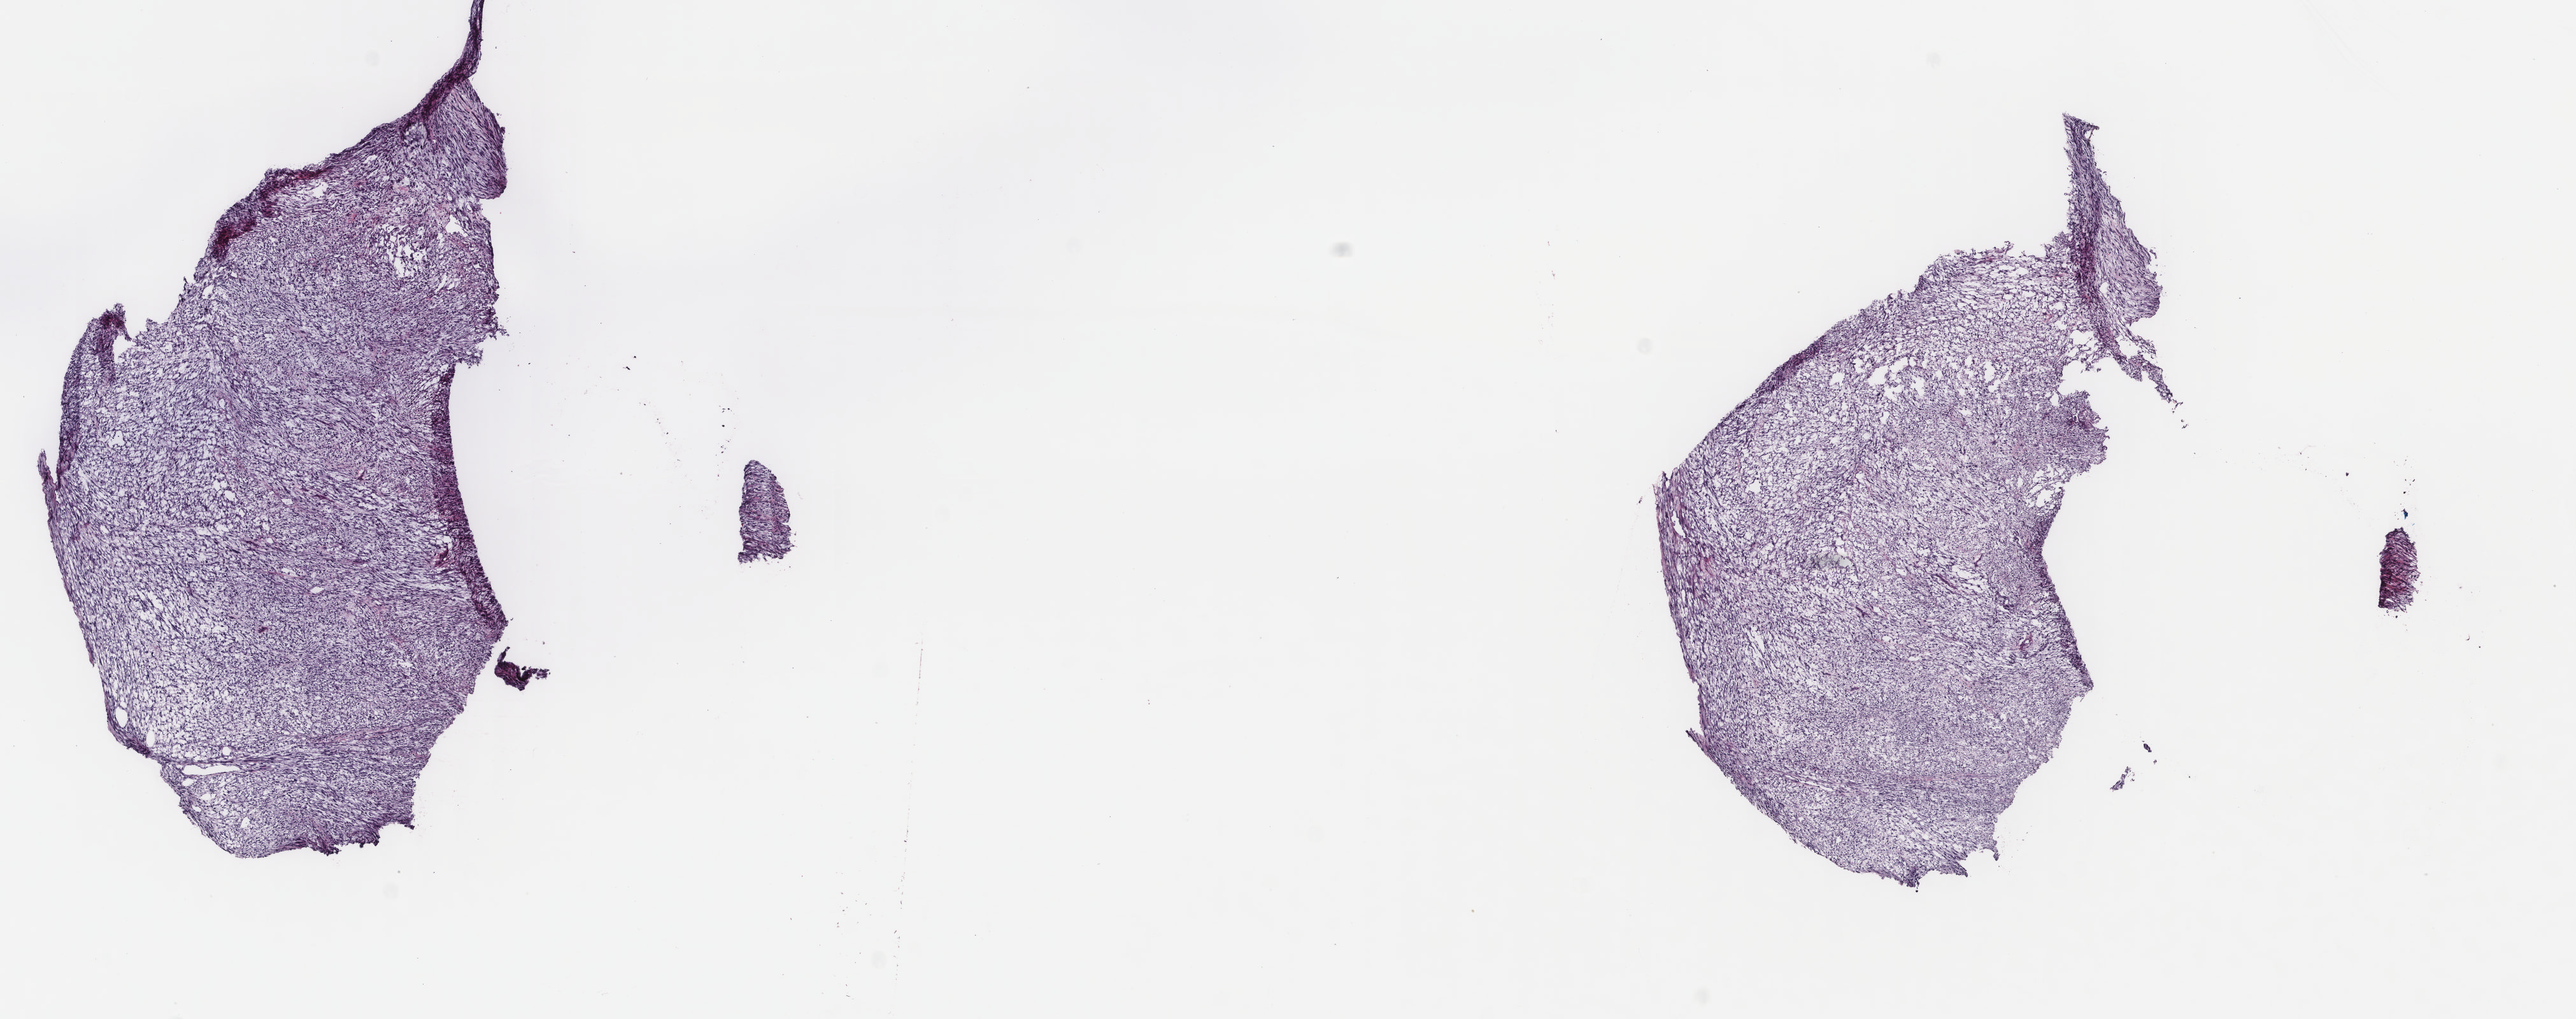
Digitized H&E-stained tissue section (whole slide) — whole scanned area (about 16.1 x 6.4 mm, slide scanned at 40x) shown as a low-resolution overview; frozen section from the top of the tissue portion; retroperitoneum and peritoneum, primary tumour sample. Female, age 65 years at initial diagnosis. Slide review estimates, as recorded: tumour cells 95%, tumour nuclei 95%, normal cells 0%, stromal cells 5%, necrosis 0%. Inflammatory infiltration, as recorded: lymphocyte infiltration 0%, monocyte infiltration 0%, neutrophil infiltration 0%.
Diagnosis: Leiomyosarcoma, NOS (retroperitoneum).